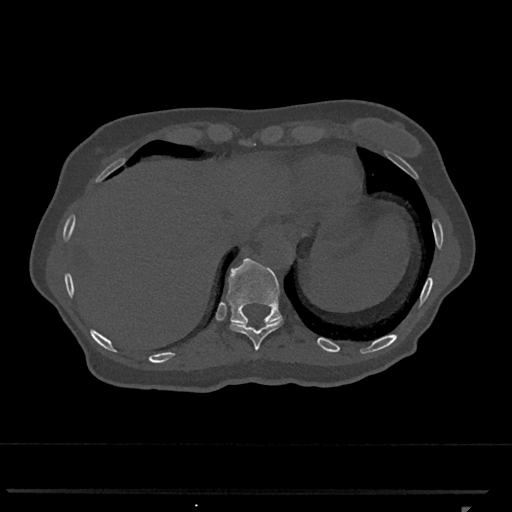
CT including the spine, one axial slice. Slice 547 of 793 in the series (ordered by position). Reconstruction kernel Br40s/3. 120 kVp. Bone window (W 1800 / L 400 HU). 0.5 mm slice thickness. 512 × 512 image matrix, field of view 380 × 380 mm. Patient: female, 62 years. Case-level facts recorded for this patient, not image findings: primary cancer: renal.
Structures marked on this image (semi-automatic segmentation, software-assisted and operator-edited):
- T10 vertebra: bounding box [x1, y1, x2, y2] px = [230, 319, 283, 351]
- T11 vertebra: [226, 258, 283, 327]